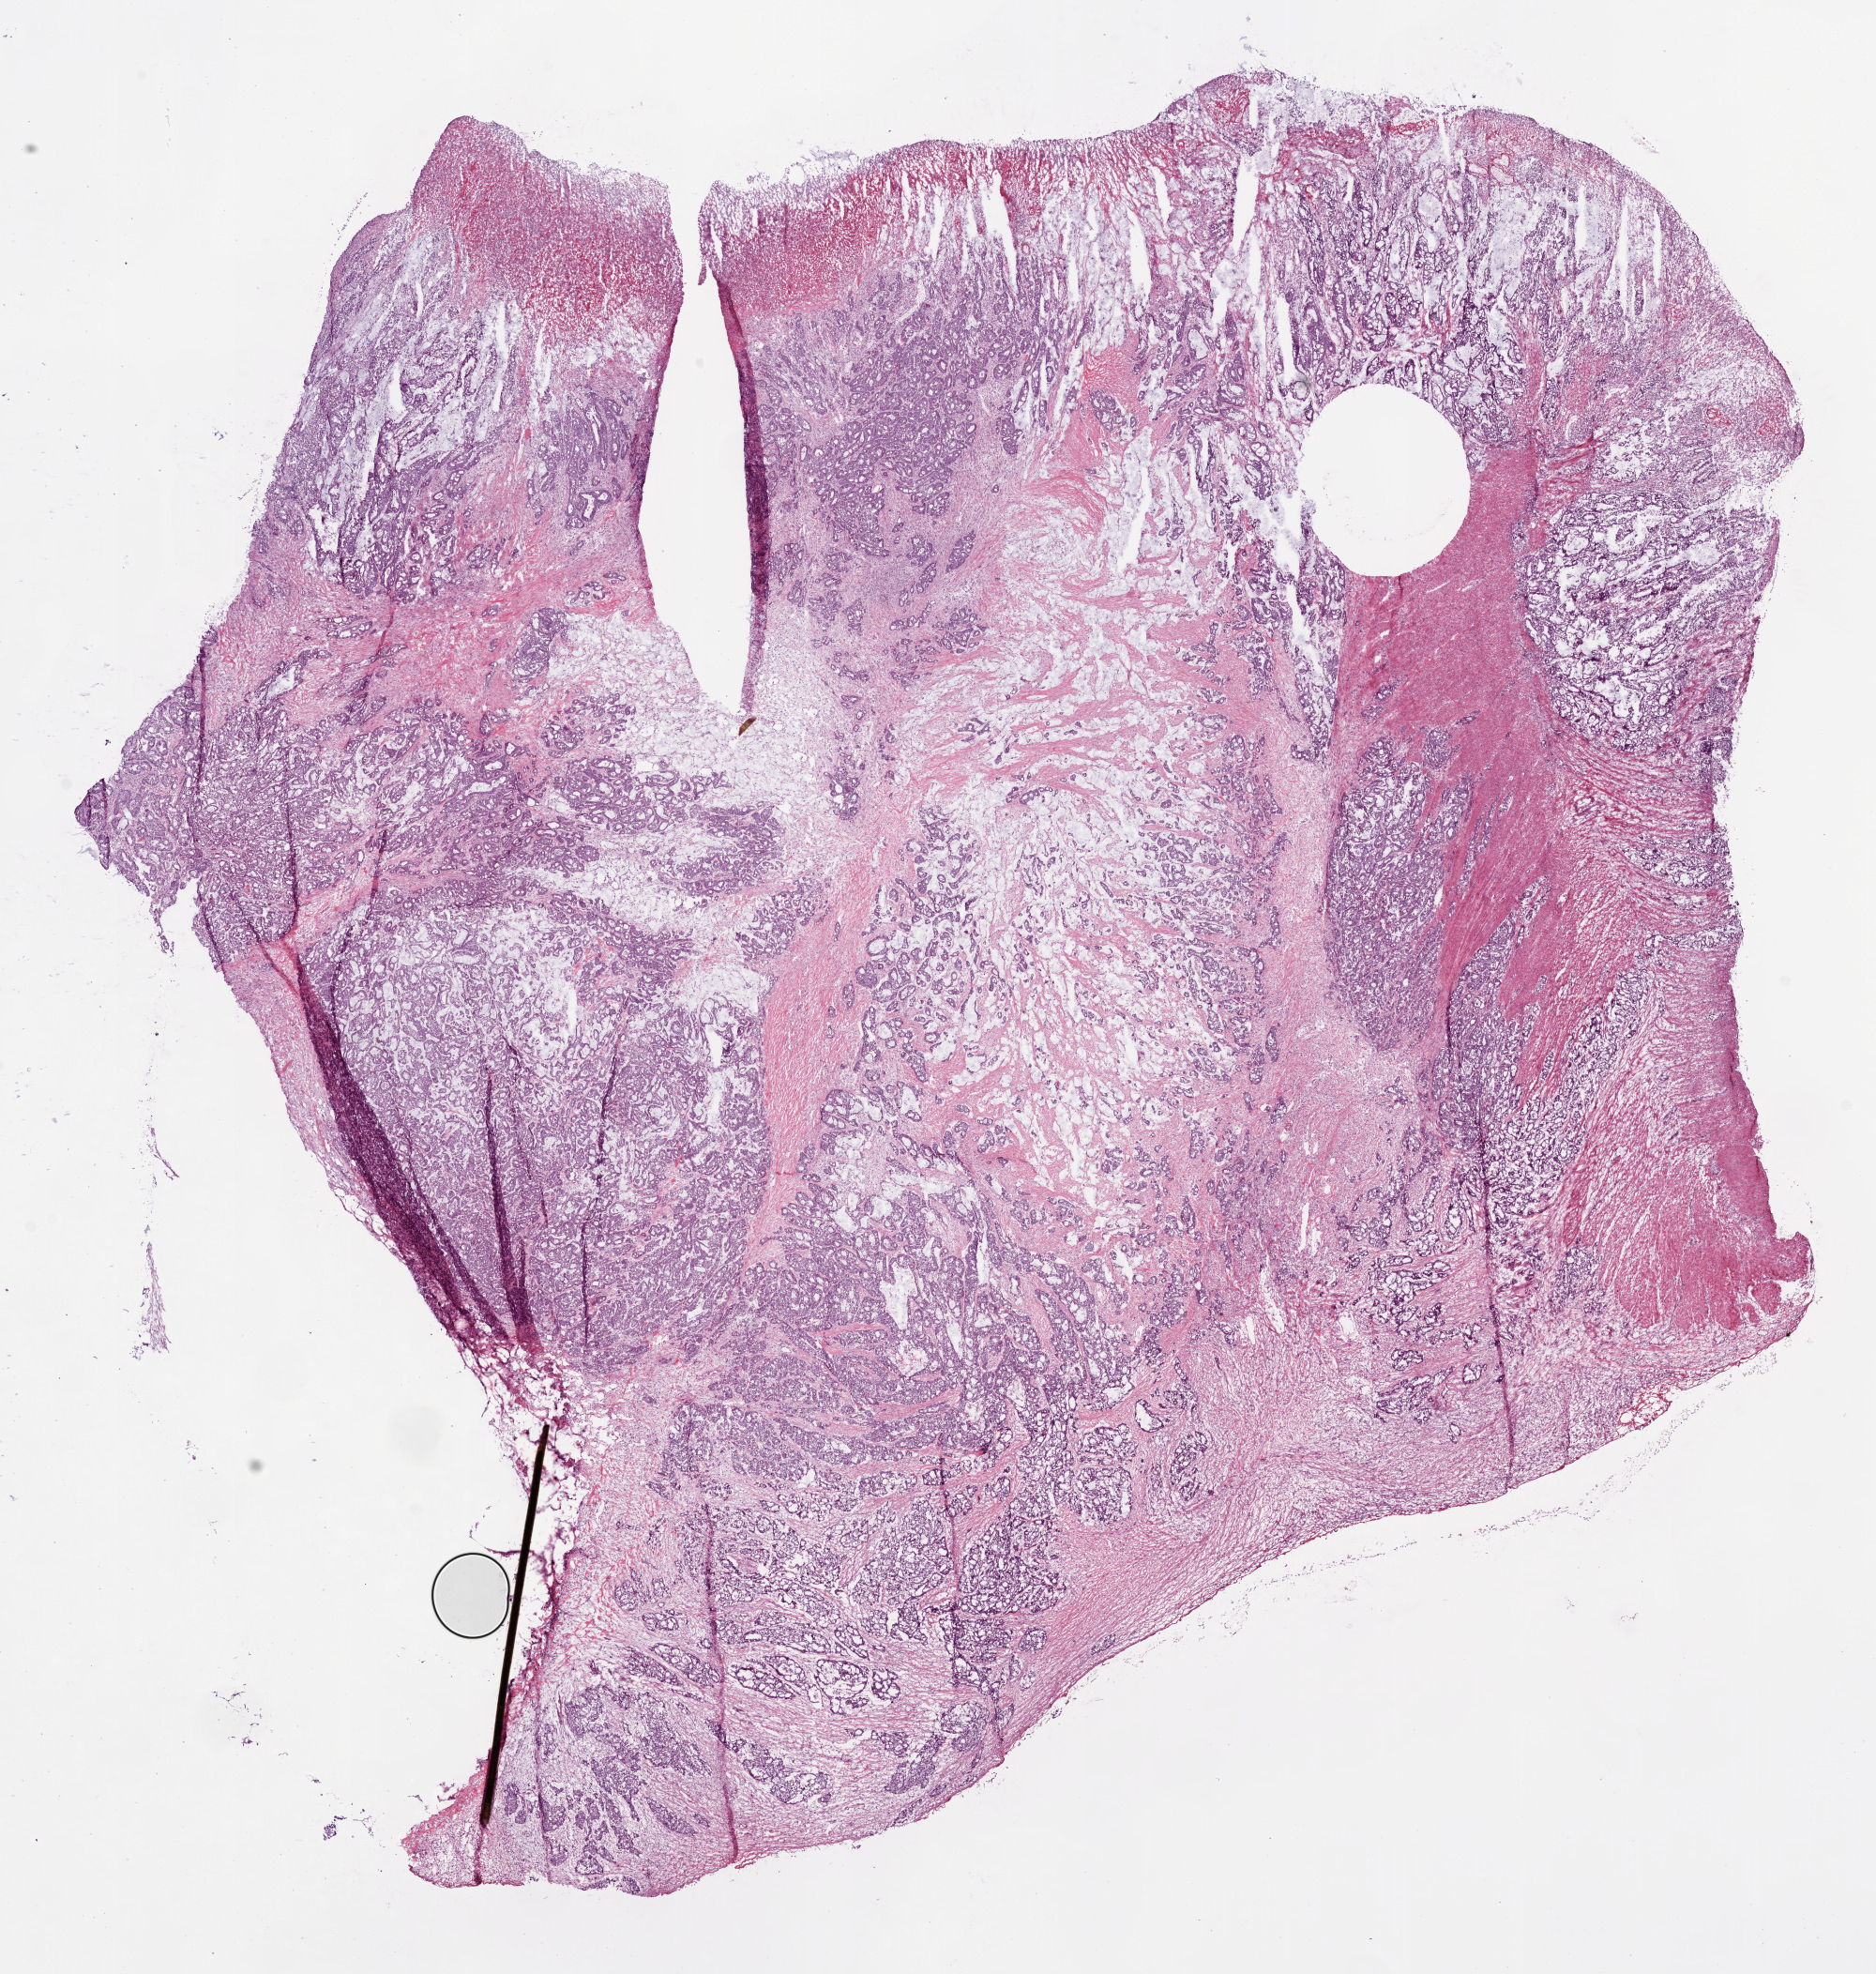
H&E-stained whole-slide image, low-resolution overview of the scanned area, about 16.0 x 16.9 mm. Frozen section. Sample: primary tumour, rectum. Male, age 51 years at initial diagnosis. Composition of this section per pathologist review: tumour cells 65%, tumour nuclei 80%, normal cells 0%, stromal cells 30%, necrosis 5%.
- AJCC pathologic stage: II (6th edition)
- histologic diagnosis: Mucinous adenocarcinoma